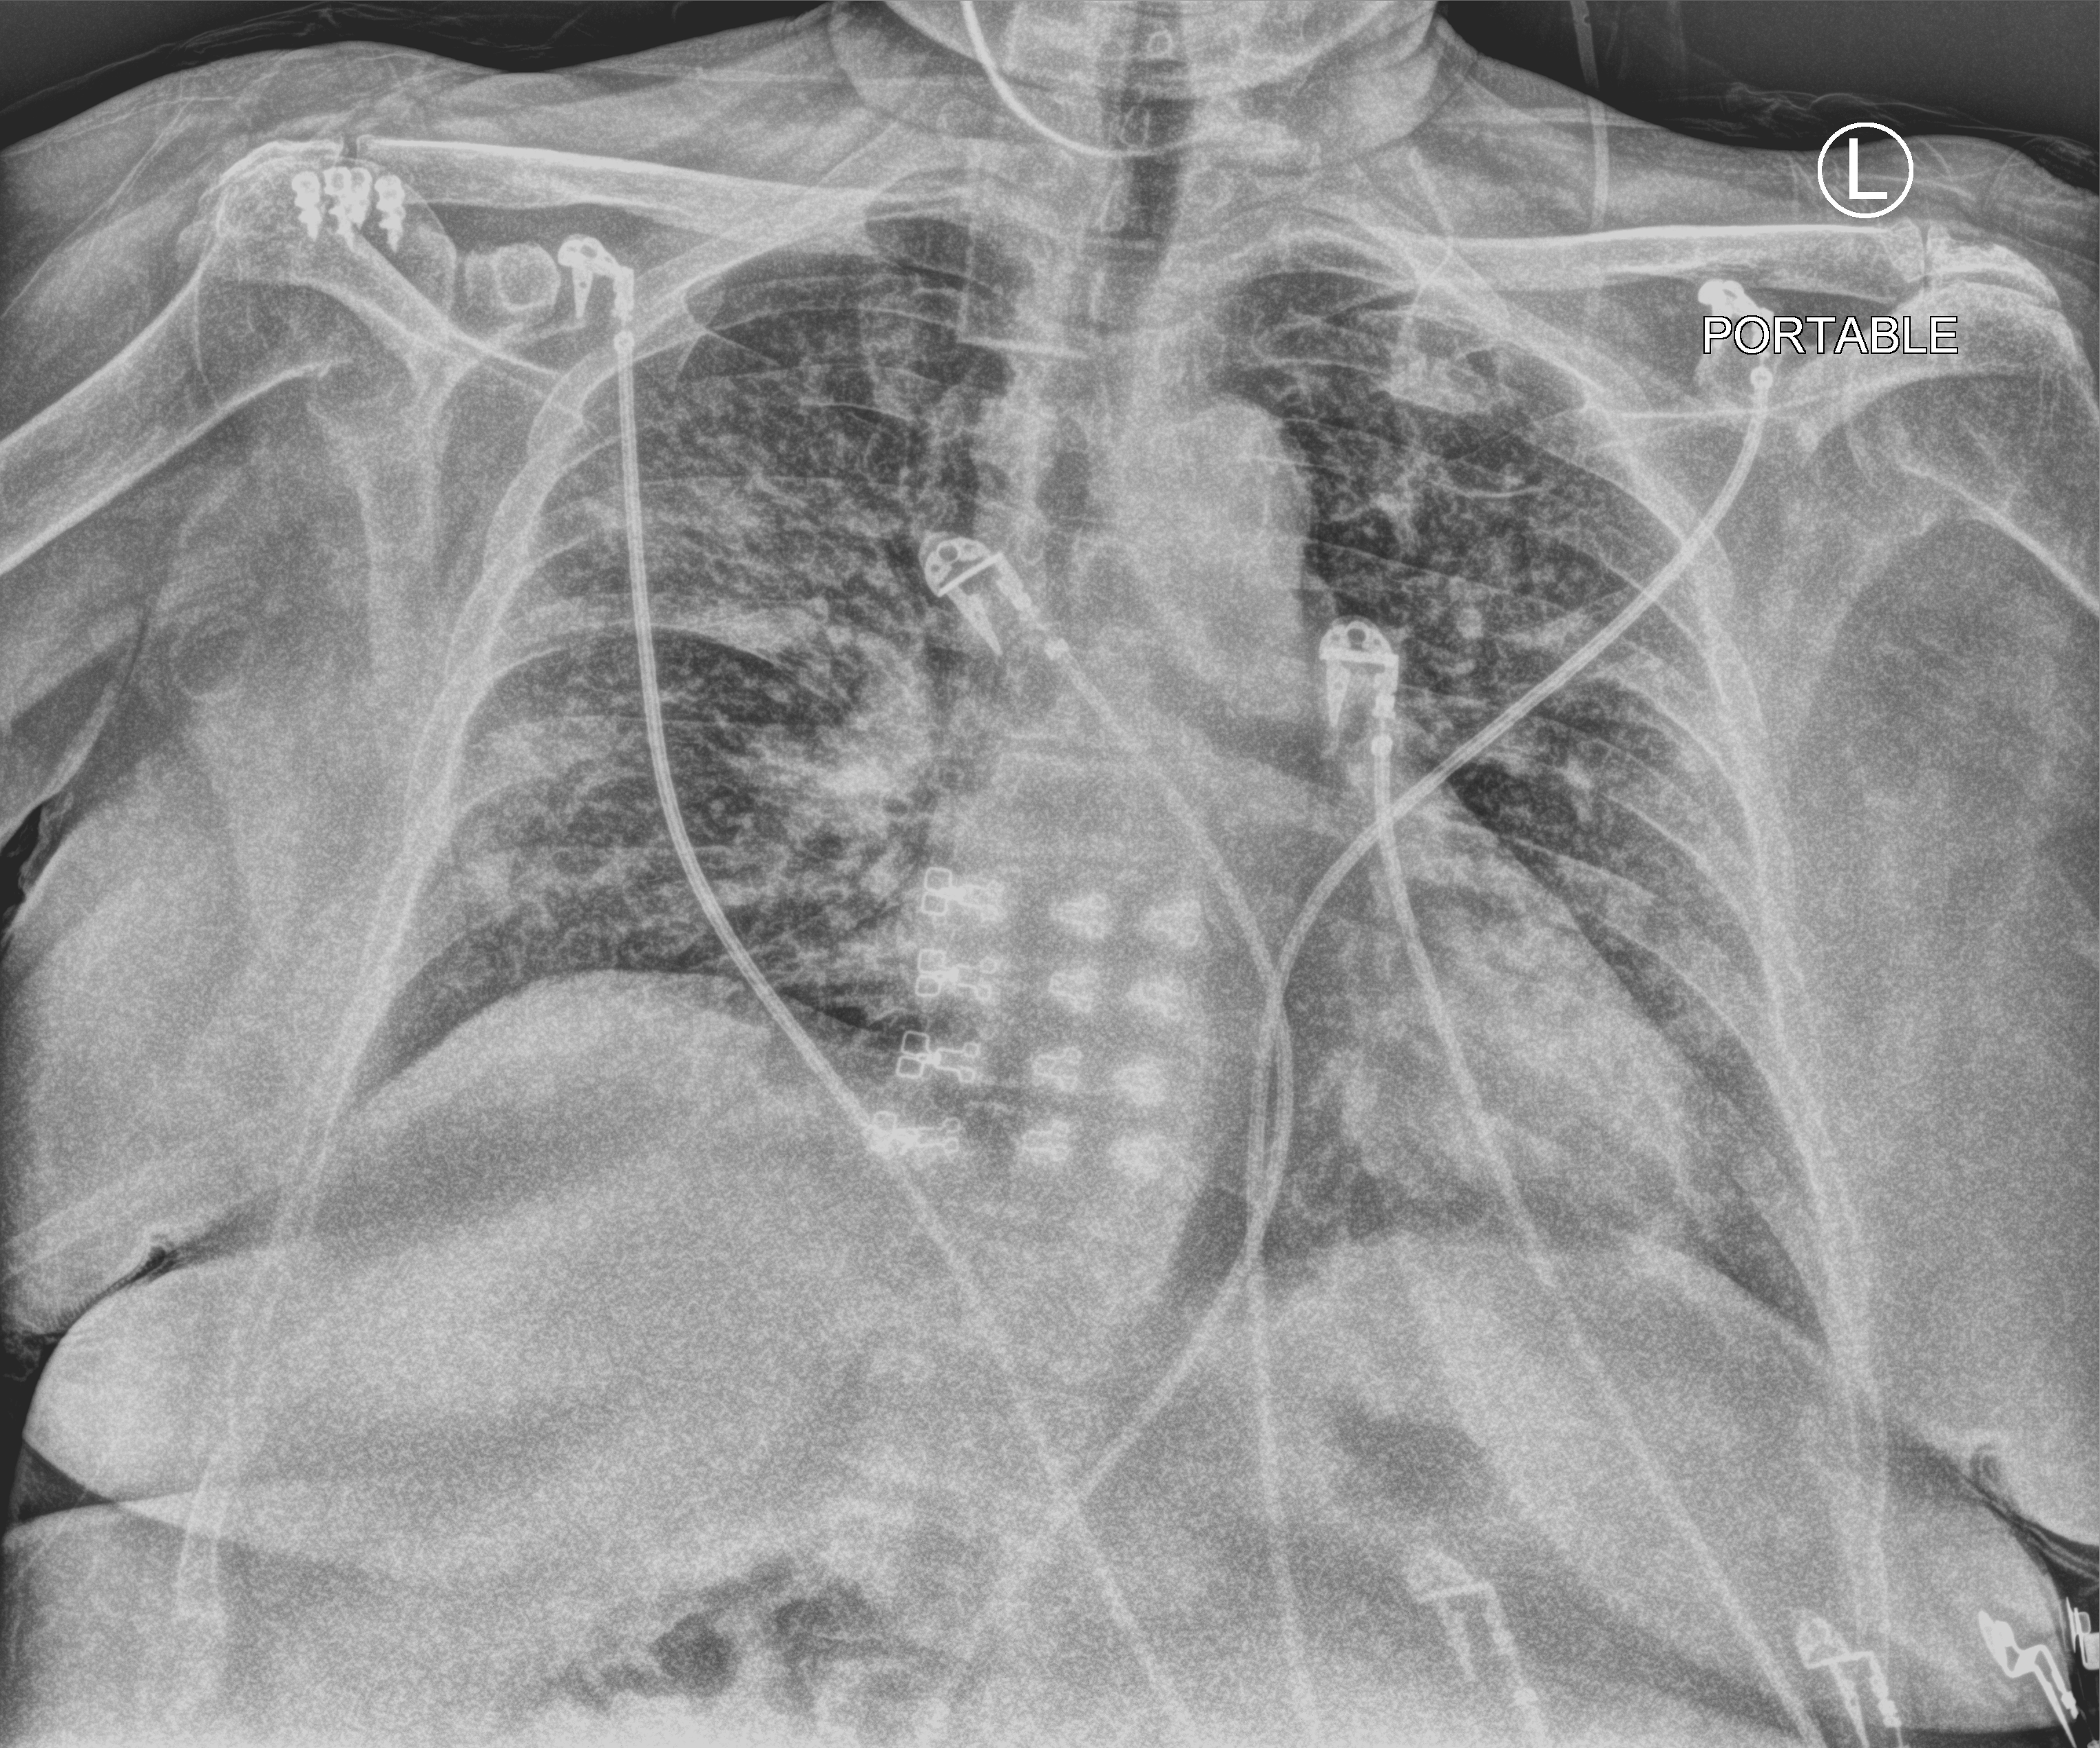
Bedside chest radiograph (computed radiography). Patient hospitalised with COVID-19; female, aged 60–74 years.
Admission-level facts for this patient (not findings on this image; timing relative to this image not recorded):
- admitted to intensive care during this hospital stay: yes
- length of hospital stay: 19 days